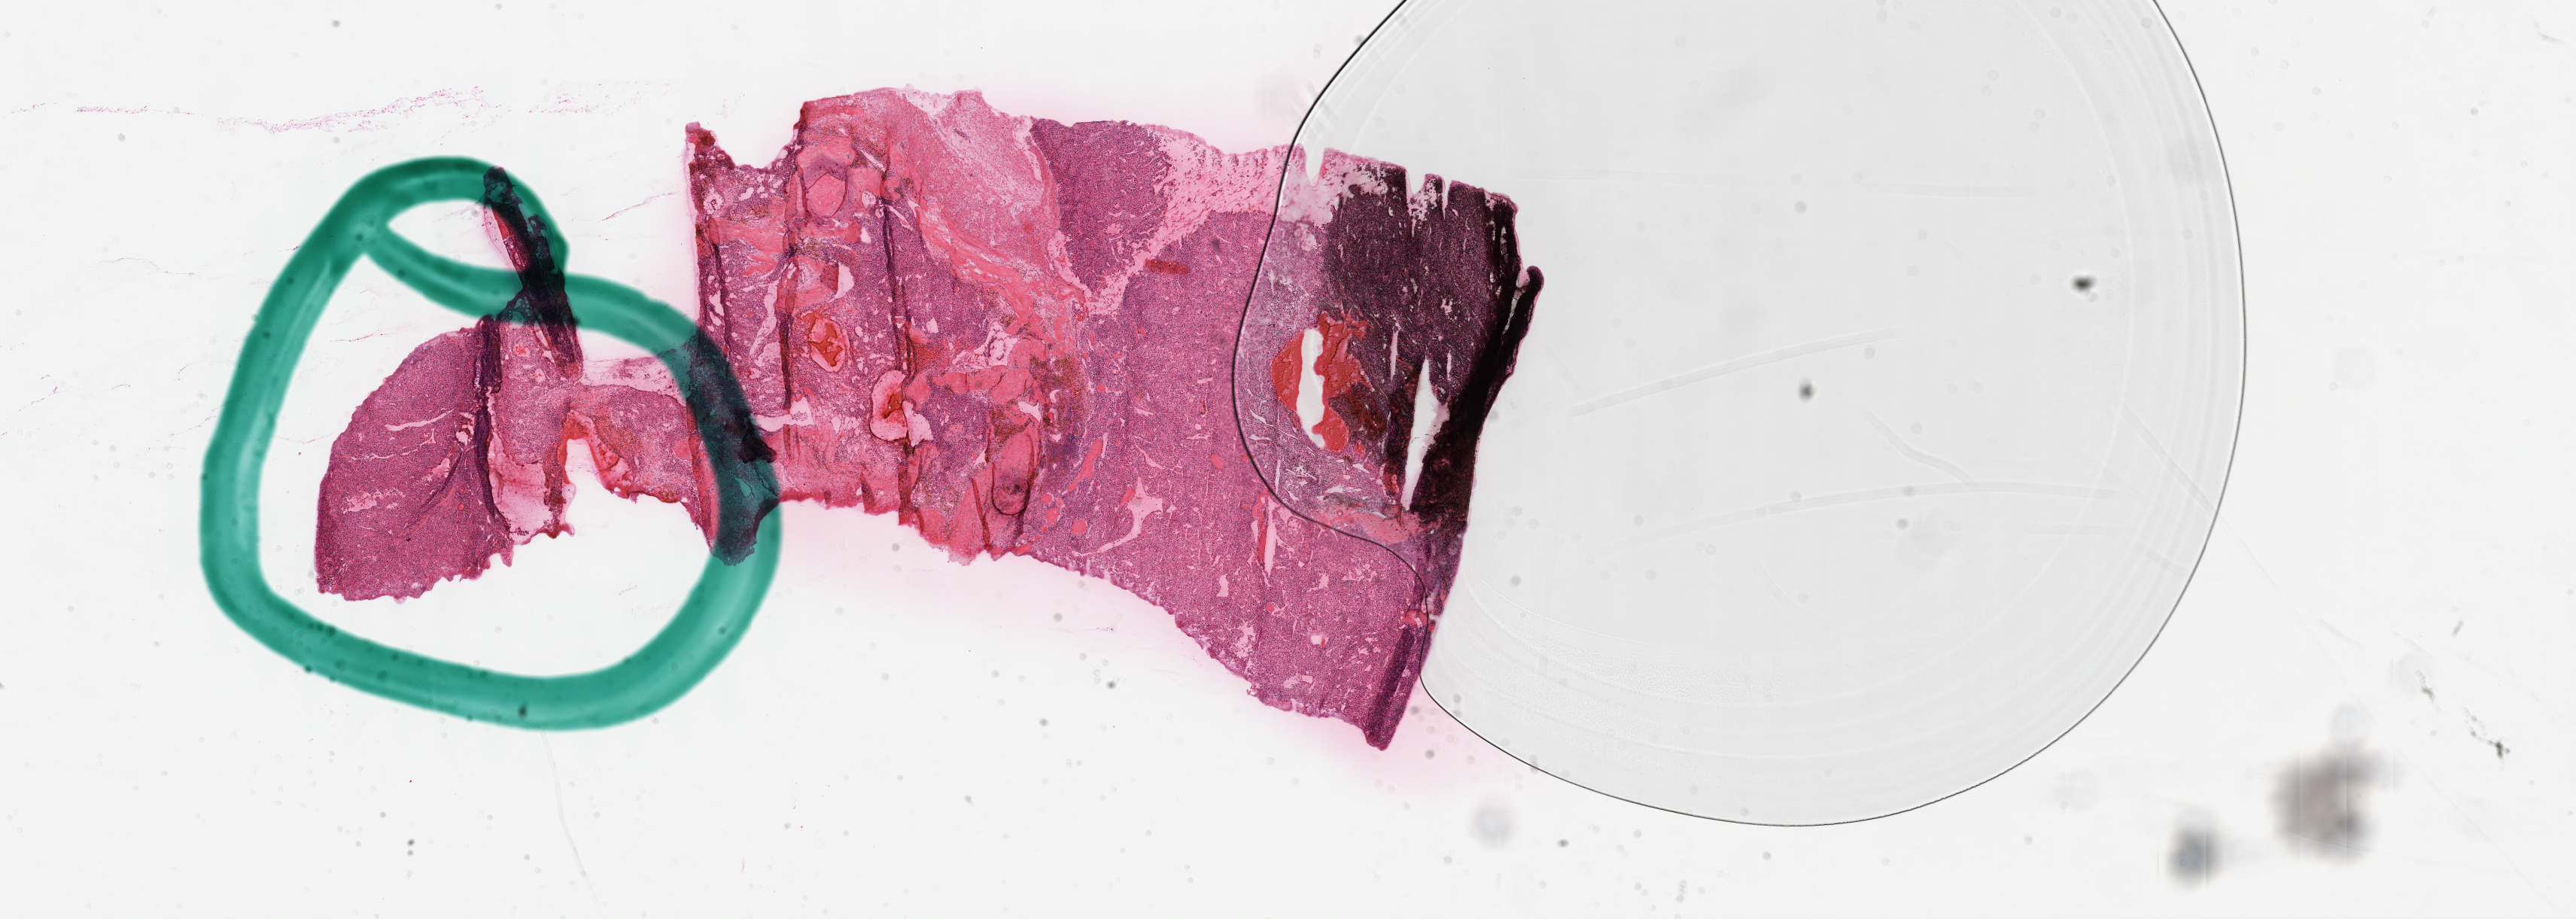
Whole-slide histology image, H&E, whole scanned area (about 27.7 x 9.9 mm) shown as a low-resolution overview, formalin-fixed paraffin-embedded (FFPE) diagnostic section, kidney, primary tumour sample. Male patient; age at initial diagnosis 47 years. Histologic grade: G3 (poorly differentiated).
* AJCC pathologic stage: III (7th edition)
* pathologic diagnosis: Clear cell adenocarcinoma, NOS
* laterality: right